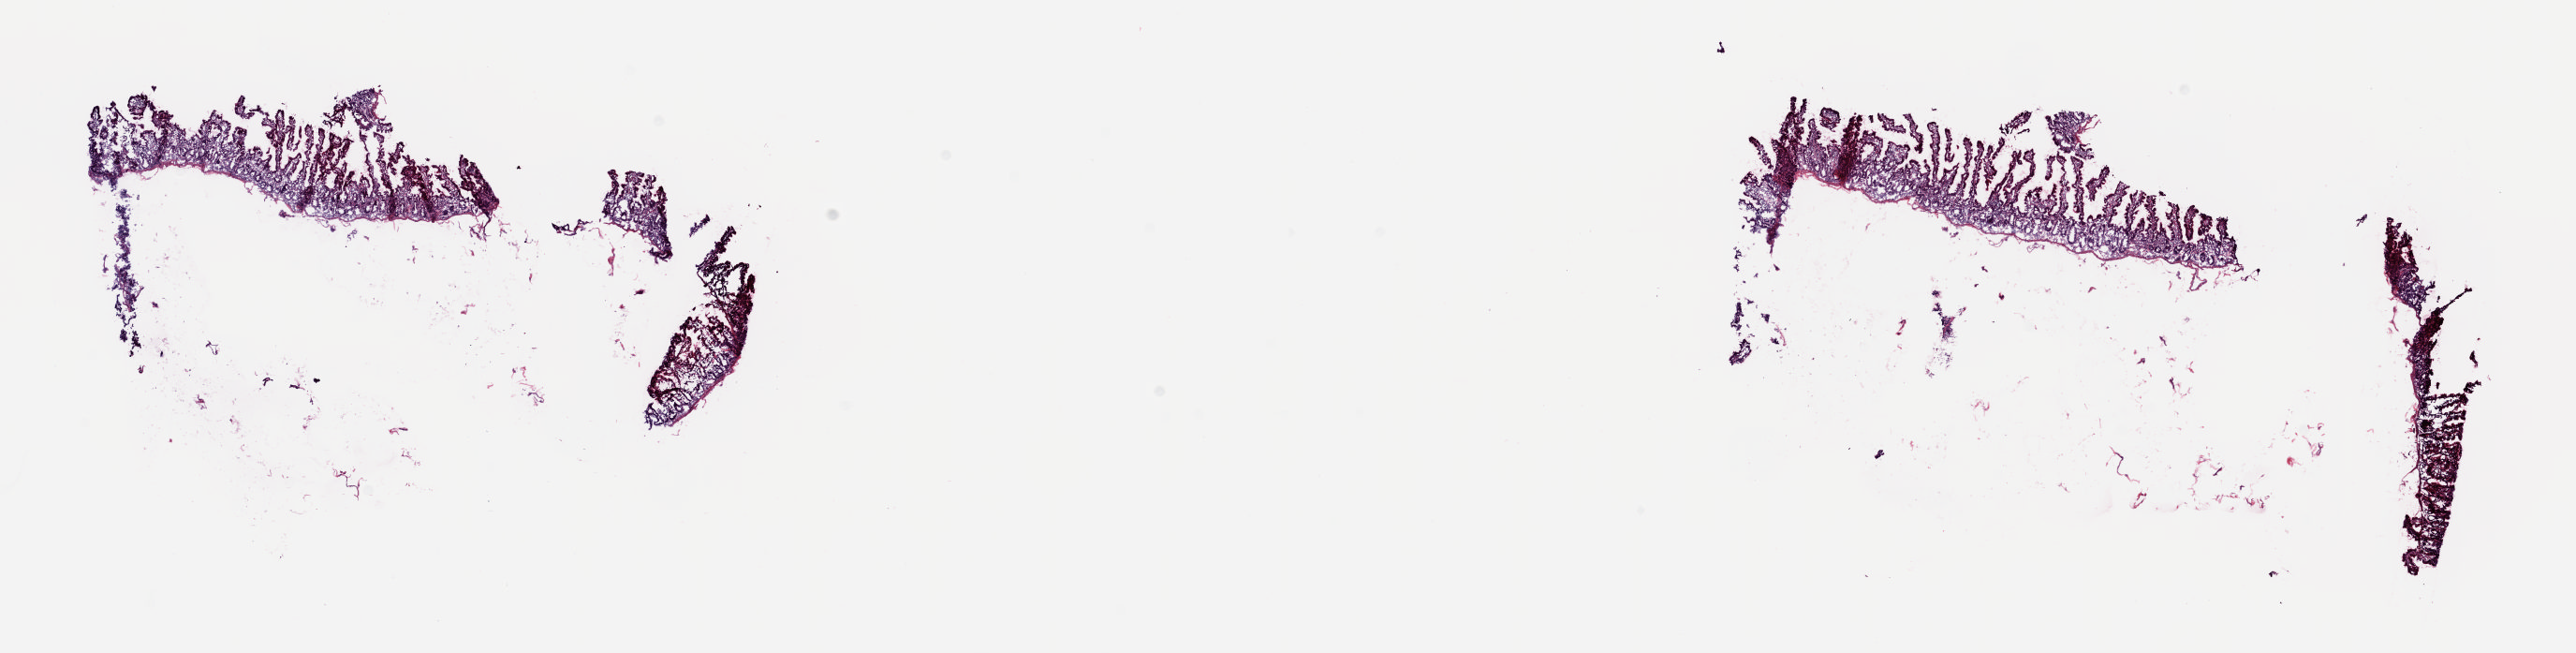
Digitized H&E-stained tissue section (whole slide), shown as a low-resolution overview of the whole scanned area (about 21.8 x 5.5 mm, acquisition: 20x scan), frozen section, pancreas, solid tissue normal (non-tumour tissue) sample. Female patient; age at initial diagnosis 81 years. Slide review estimates, as recorded: tumour cells 0%, tumour nuclei 0%, normal cells 100%, stromal cells 0%, necrosis 0%. Inflammatory infiltration, as recorded: lymphocyte infiltration 10%, monocyte infiltration 0%, neutrophil infiltration 1%.
• this section: solid tissue normal (non-tumour) sample from the same patient
• patient diagnosis: Infiltrating duct carcinoma, NOS